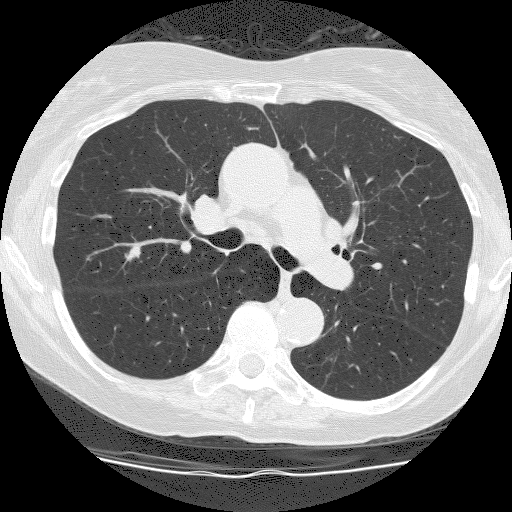
Low-dose screening chest CT, axial slice, second screening round (one year after baseline), lung window (W 1500 / L -600 HU), slice 69 of 186 in the series, 512 × 512 image matrix, field of view 300 × 300 mm. Female participant, aged 66 years at enrolment. Former smoker at enrolment.
- Lesion marked by an expert reader, bounding box <107,231,158,278> (left, top, right, bottom; pixels).
- The screening reader recorded 2 non-calcified nodules or masses ≥4 mm on this exam (right upper lobe, right lower lobe); which of them this box marks is not recorded.
- Official screen result: positive, other.
- Later outcome: lung cancer diagnosed 209 days after this screen — squamous cell carcinoma, NOS, right upper lobe, stage IIIA (AJCC 6th edition), 10 mm at pathology.